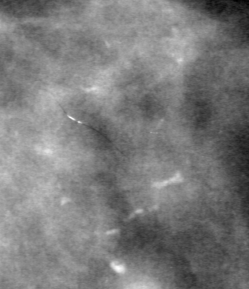
Cropped region of a digitized screen-film mammogram centred on a radiologist-marked abnormality, right breast, MLO view, BI-RADS breast density category 2 (scale 1–4).
Marked abnormality: calcifications, morphology pleomorphic, distribution clustered; BI-RADS assessment category 4; pathology (as recorded): malignant.